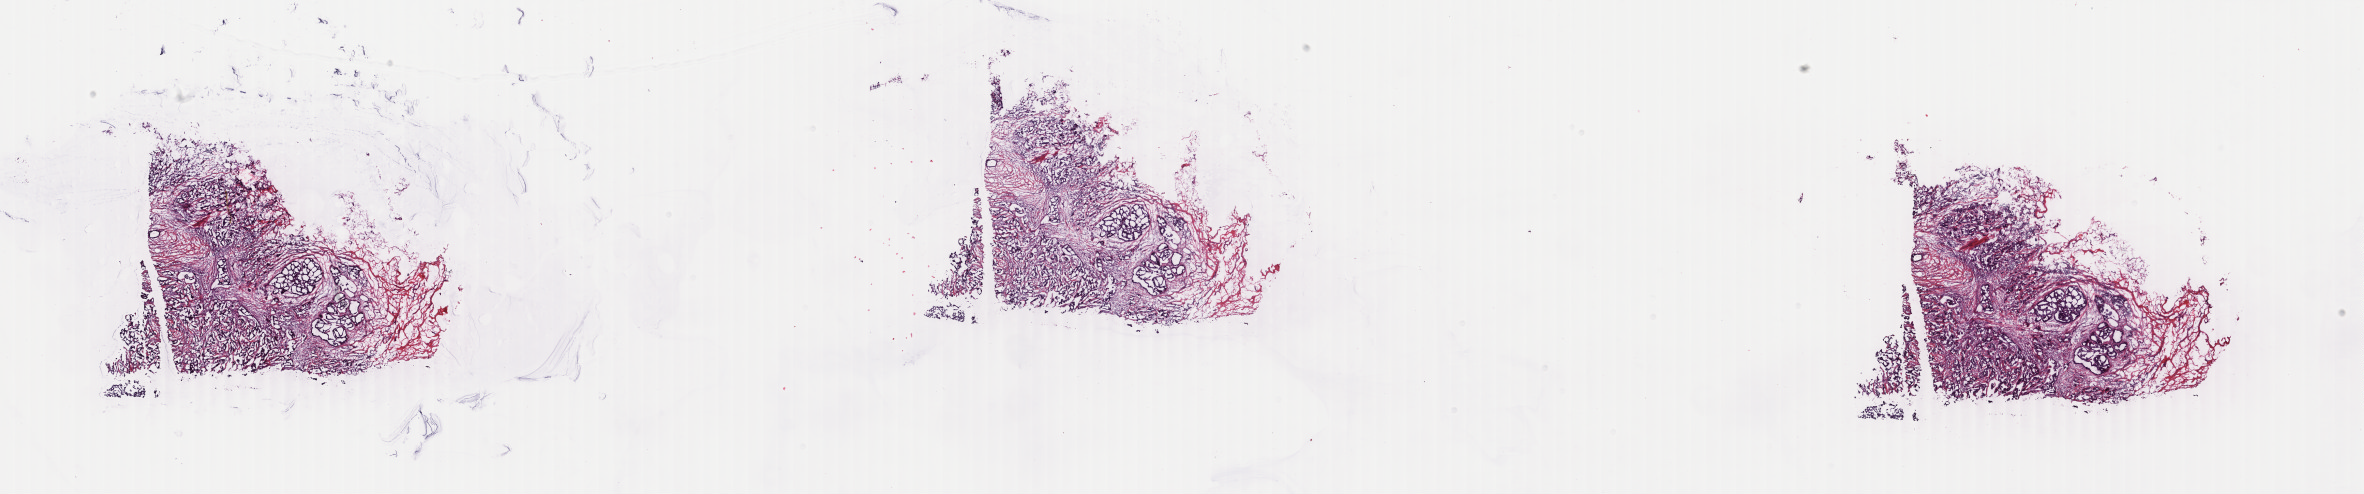
Digitized H&E tissue section (whole slide) — a low-resolution overview of the entire scanned area, about 37.6 x 7.9 mm; frozen section from the bottom of the tissue portion; primary tumour sample from the breast. Female patient; age at initial diagnosis 49 years. Slide review estimates, as recorded: tumour cells 80%, tumour nuclei 80%, normal cells 3%, stromal cells 17%, necrosis 0%. Infiltration values recorded for this section: lymphocyte infiltration 1%, monocyte infiltration 0%, neutrophil infiltration 0%.
Laterality: right. Diagnosis: Infiltrating duct carcinoma, NOS. AJCC pathologic stage: IIB.